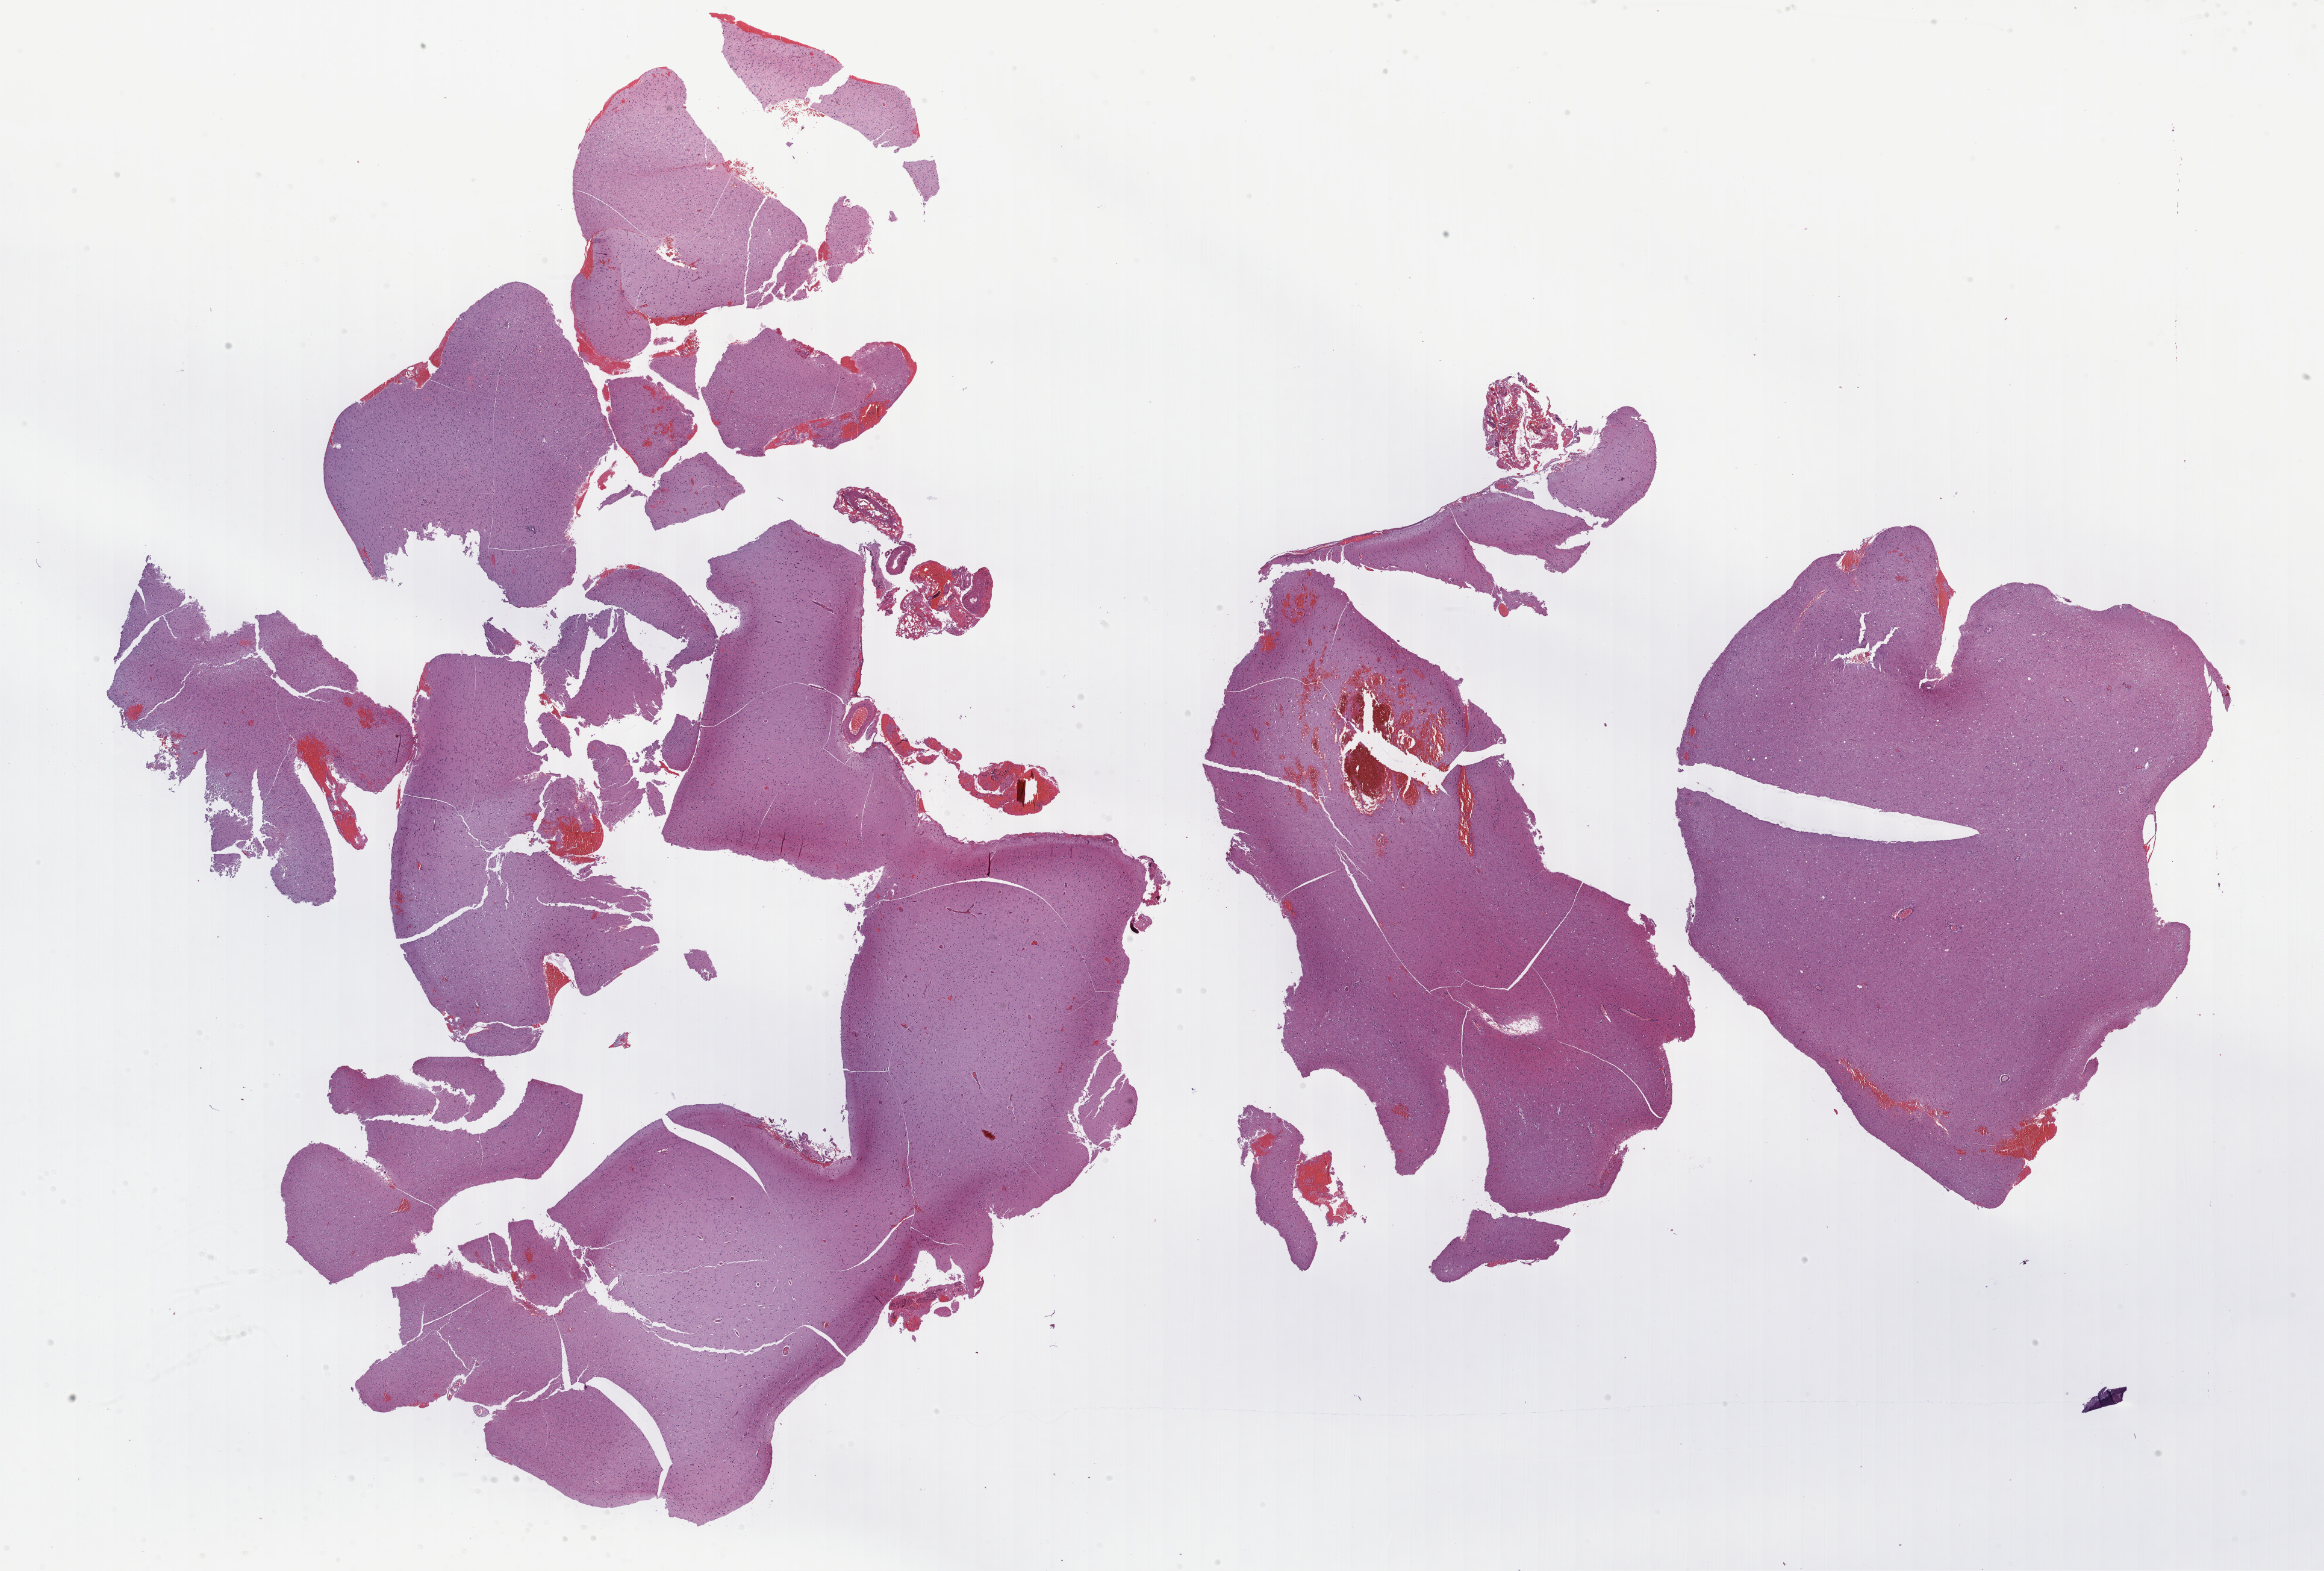
H&E whole-slide image — shown as a low-resolution overview of the whole scanned area (about 31.2 x 21.1 mm, from a 40x scan); formalin-fixed paraffin-embedded (FFPE) diagnostic section; brain, primary tumour sample. Male, age 58 years at initial diagnosis. Histologic grade: G3 (poorly differentiated).
Diagnosis: Astrocytoma, anaplastic. Laterality: right.